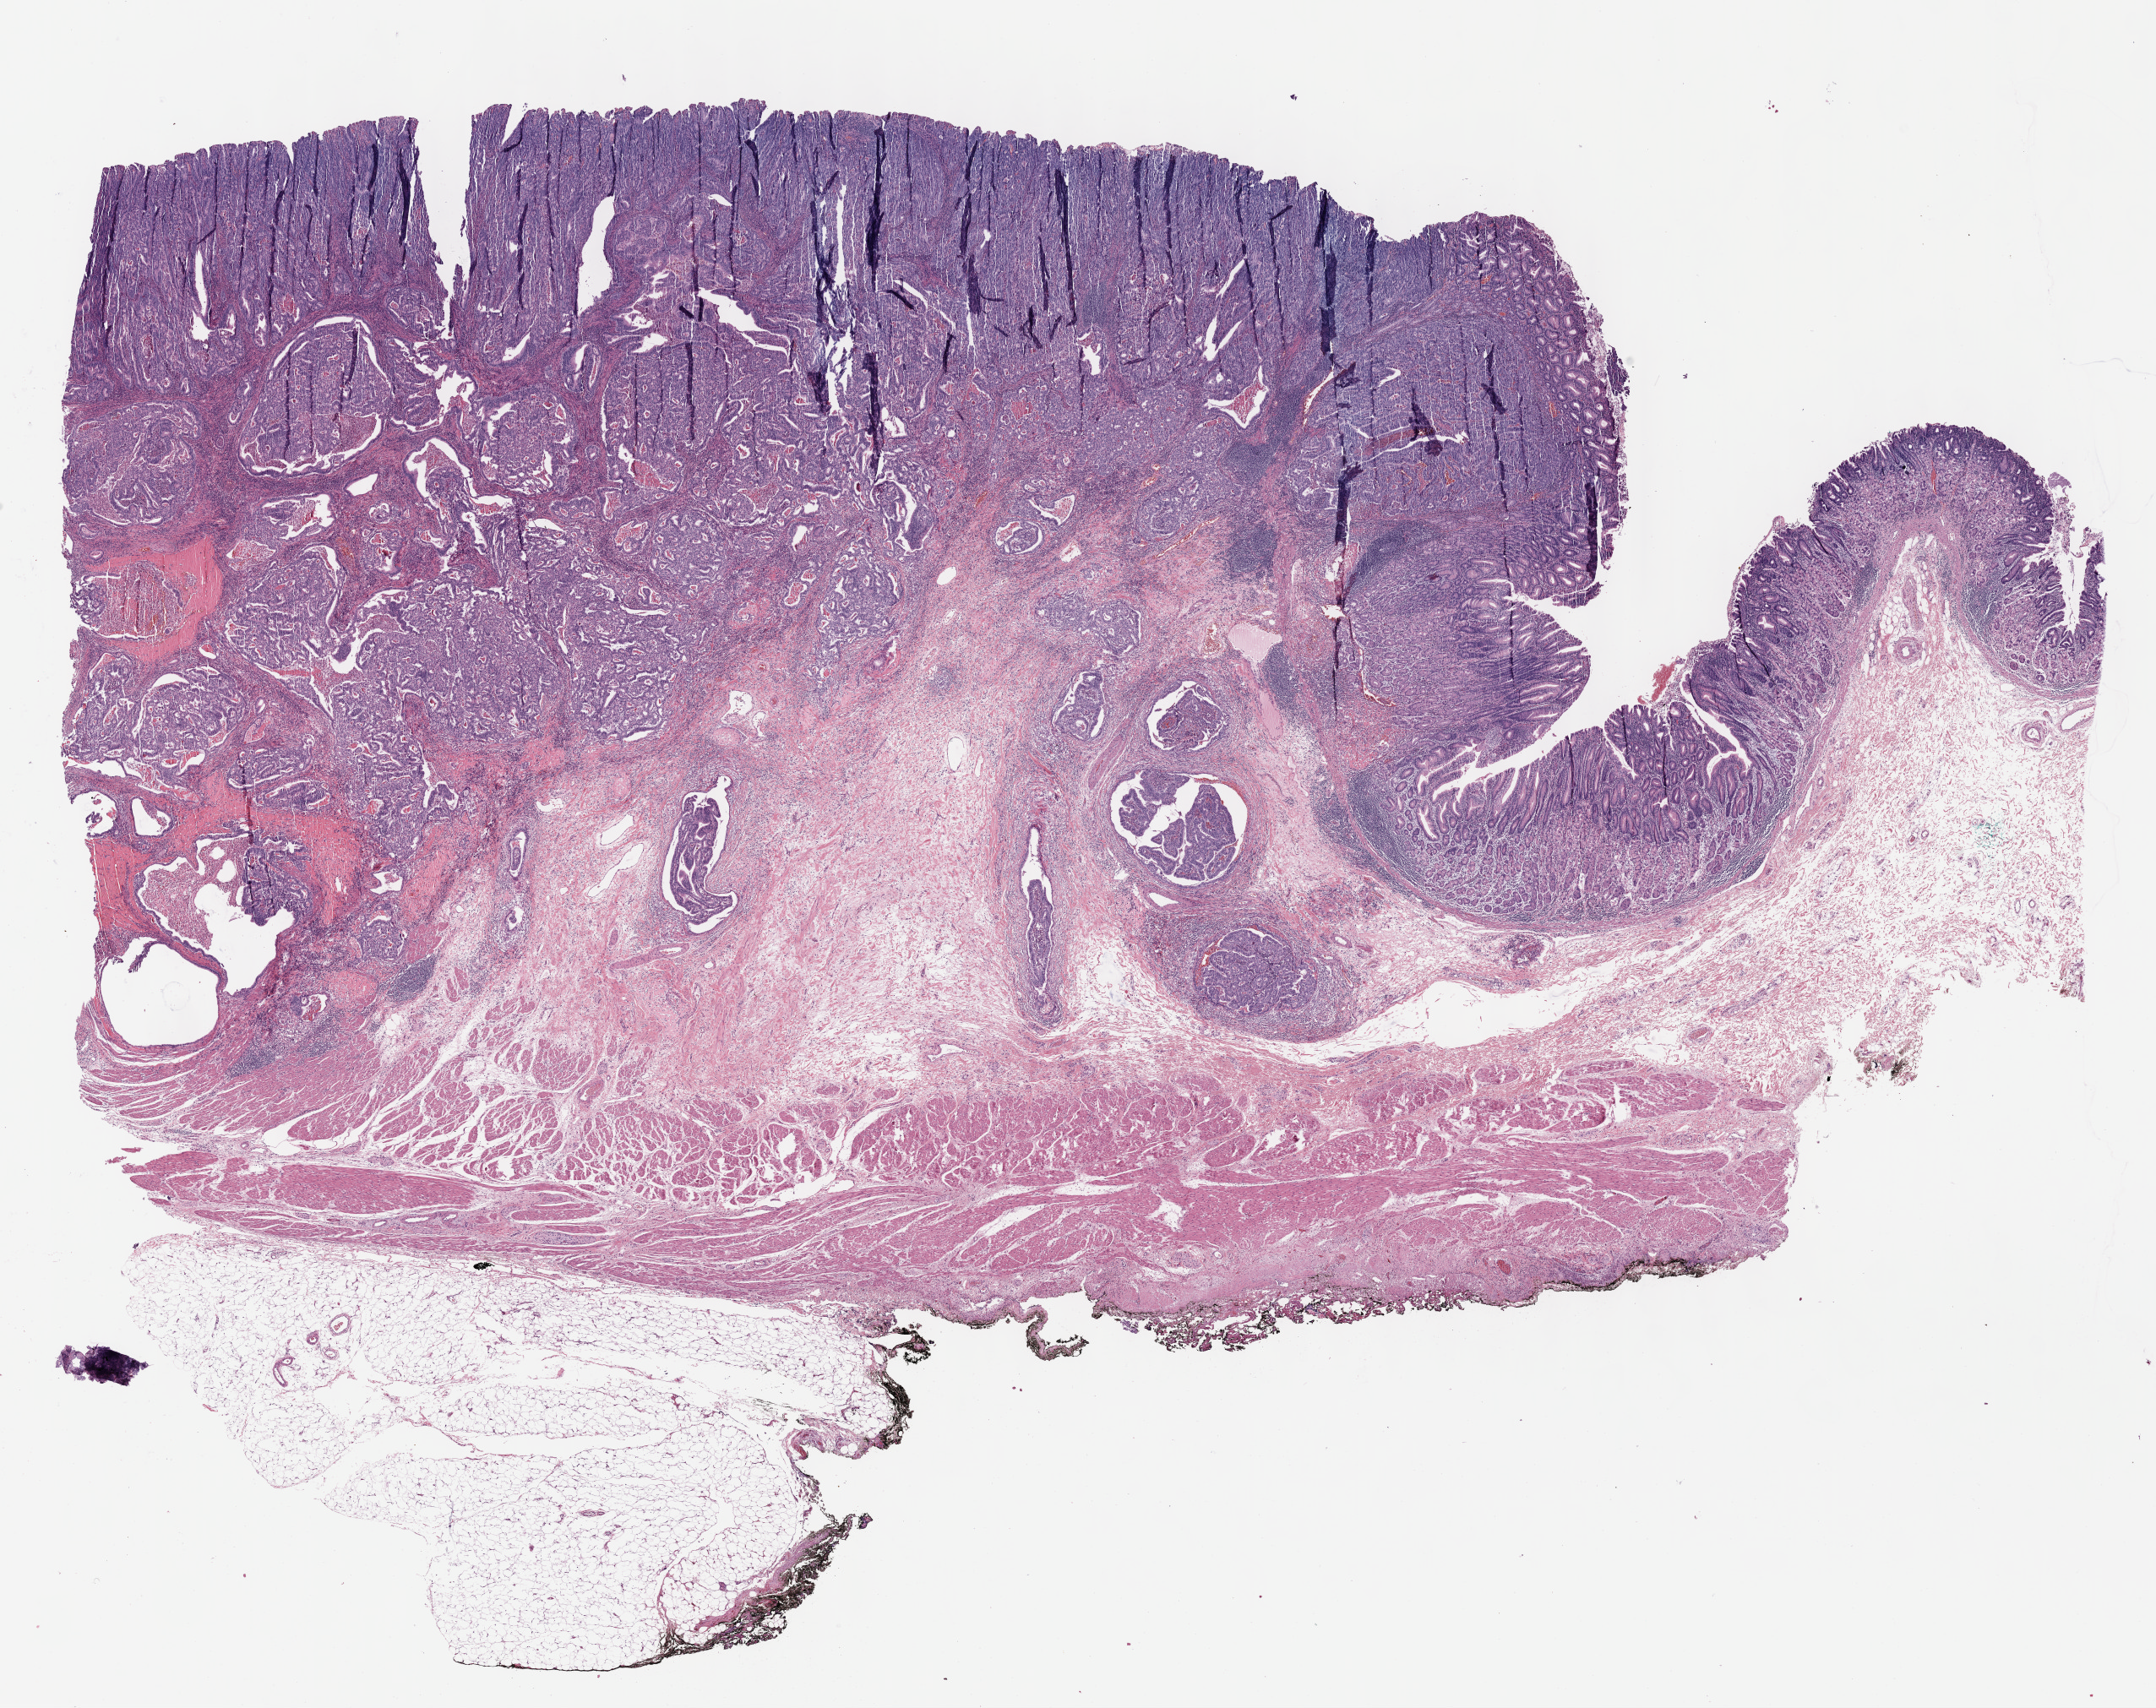
Whole-slide histology image, Hematoxylin and eosin (H&E) stained — low-resolution overview of the scanned area, about 20.6 x 16.3 mm, formalin-fixed paraffin-embedded (FFPE) diagnostic section, sample: primary tumour, stomach. Patient: male, age at initial diagnosis 35 years. Histologic grade: G2 (moderately differentiated).
* lymph nodes positive (case pathology): 6 of 37 examined
* histologic diagnosis: Adenocarcinoma, NOS (cardia, NOS)
* AJCC pathologic stage: IIIA (7th edition)